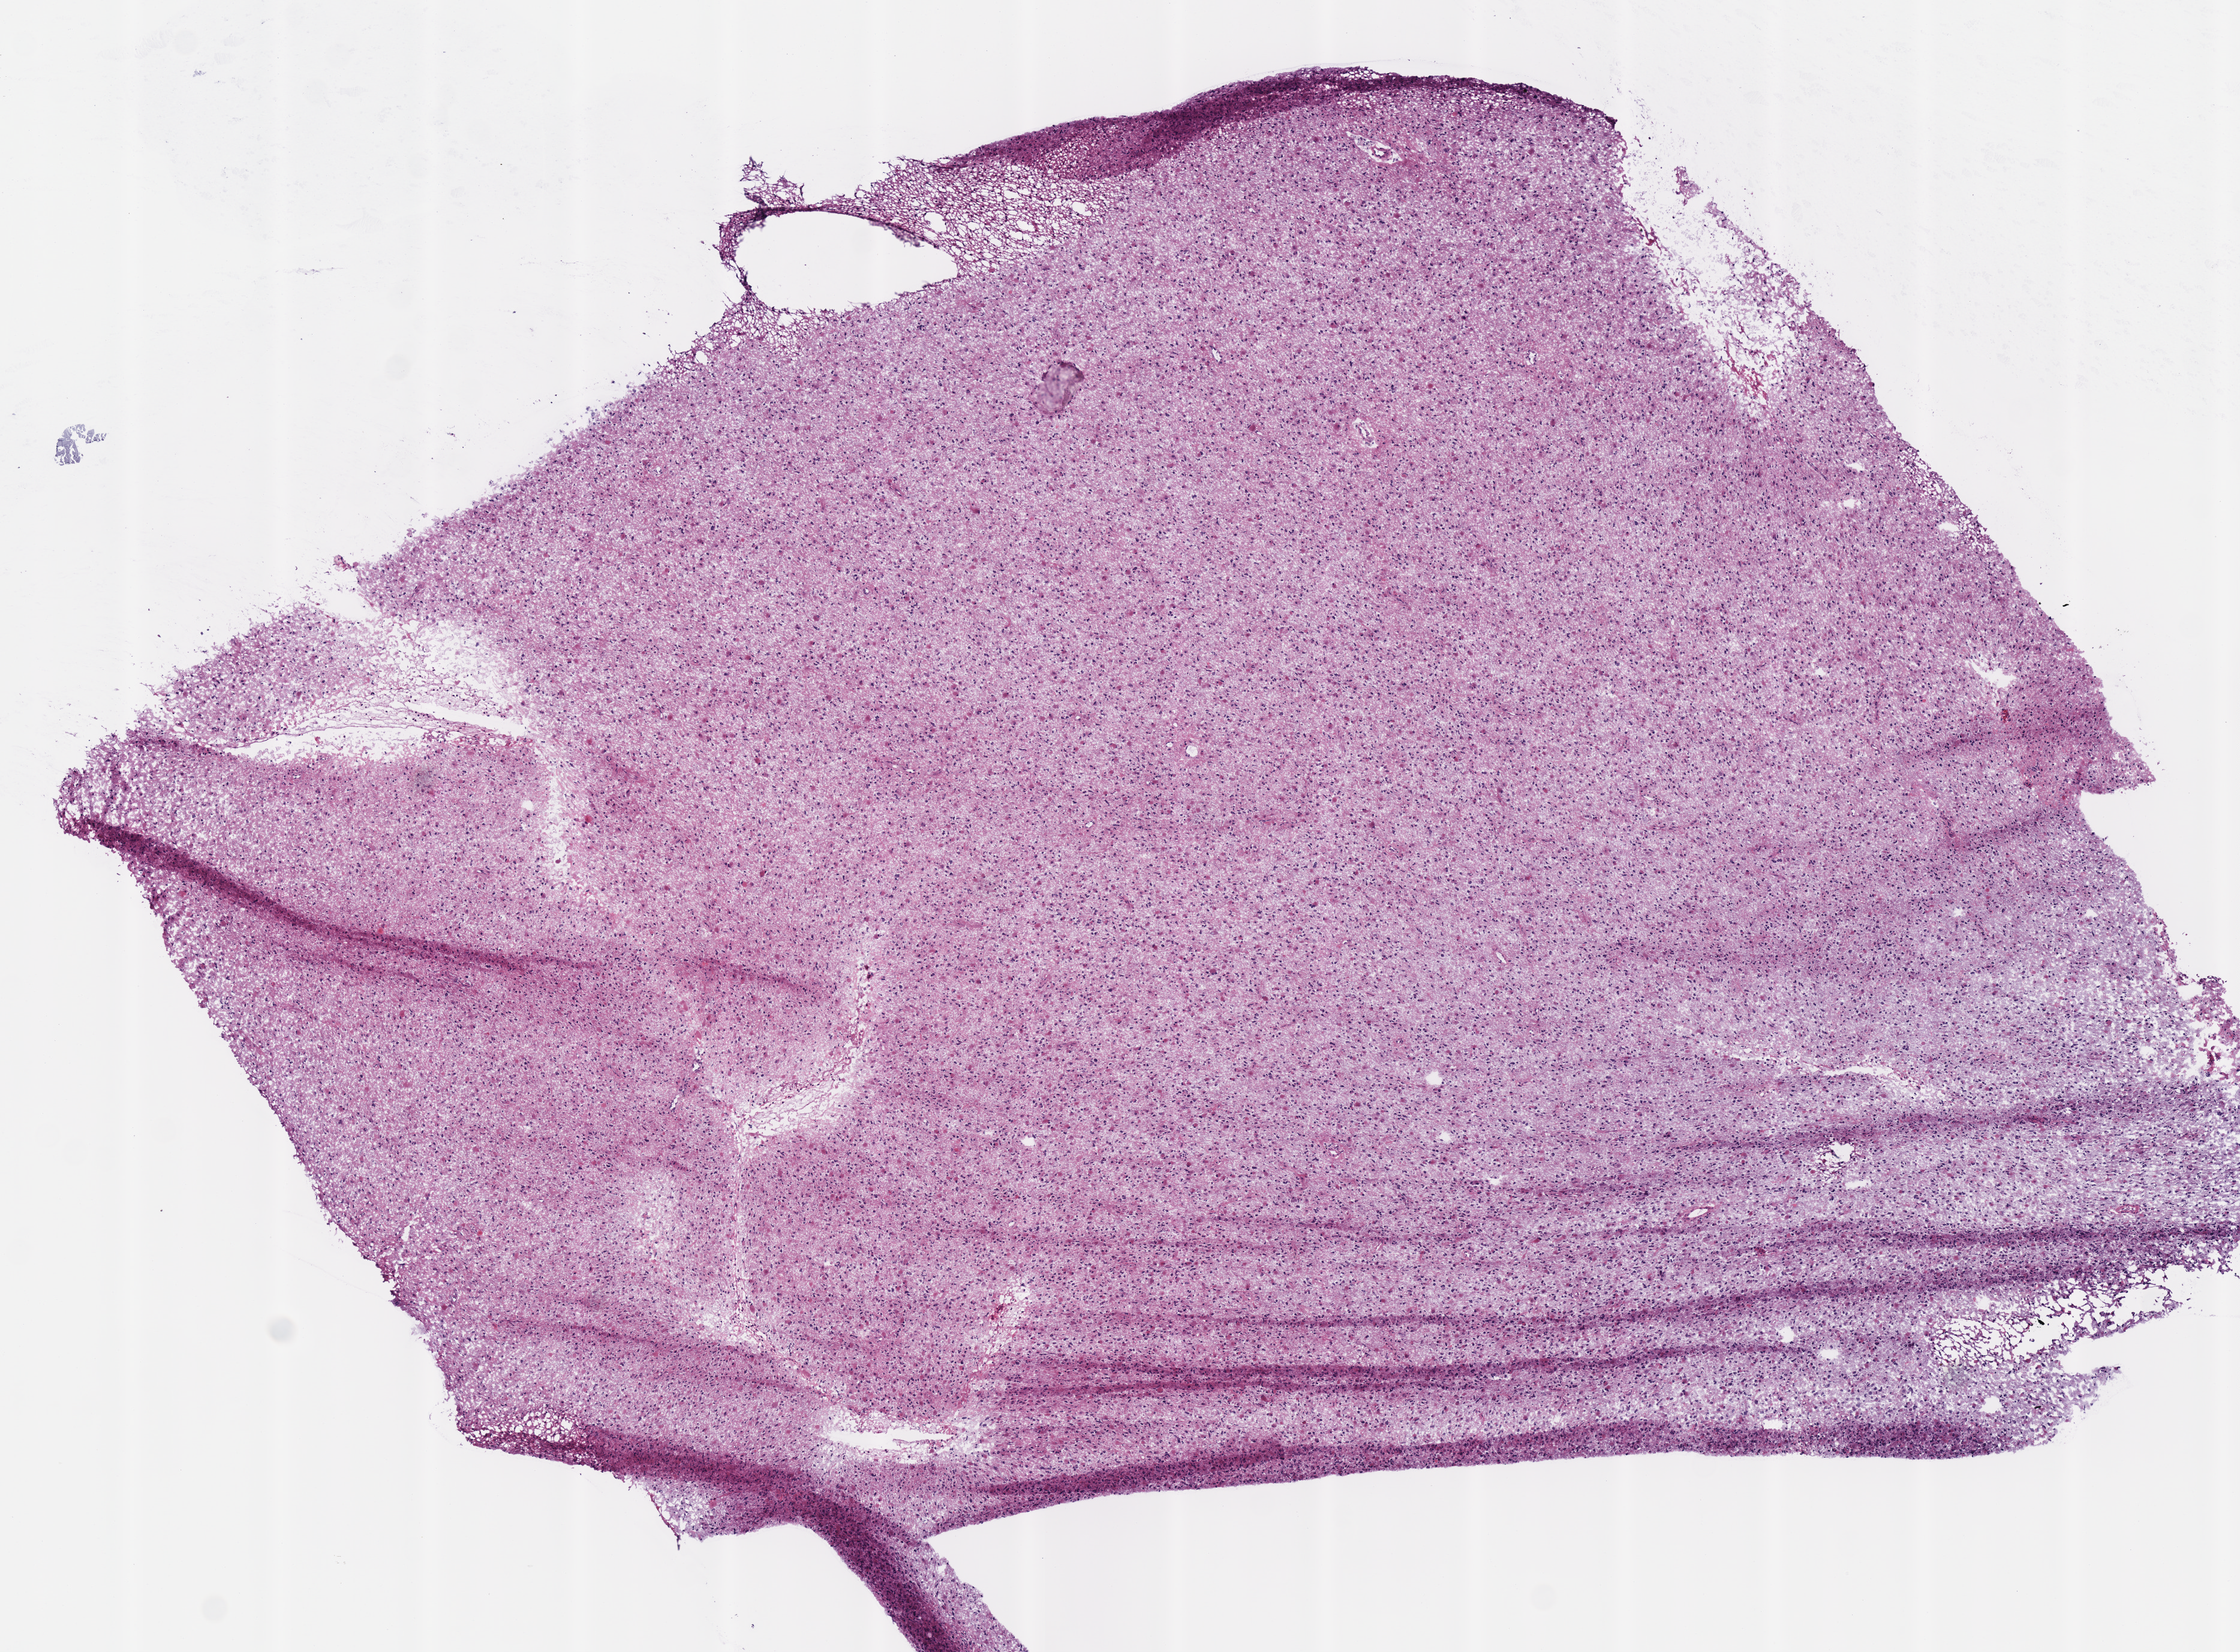
Hematoxylin and eosin (H&E) stained whole-slide image — shown as a low-resolution overview of the whole scanned area (about 7.3 x 5.4 mm, from a 40x scan). Frozen section from the top of the tissue portion. Primary tumour sample from the brain. Patient: female, age at initial diagnosis 29 years. Histologic grade: G3 (poorly differentiated). Pathologist review of this section (percent, as recorded): tumour cells 100%, tumour nuclei 80%, normal cells 0%, stromal cells 0%, necrosis 0%.
* diagnosis: Astrocytoma, anaplastic
* laterality: left